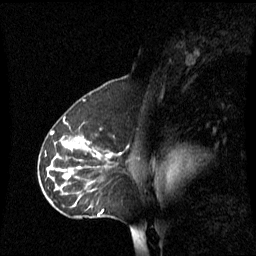
Breast MRI (dynamic contrast-enhanced), one sagittal slice; position 39 of 60 along the scan axis; dynamic contrast-enhanced series, image 2 of 3 at this slice position (ordered by acquisition); 1.5 T; TE 4.2 ms, TR 8.4 ms; 256 × 256 image matrix. Female patient, age 45 years. Case-level facts recorded for this patient, not image findings: setting: breast cancer imaged before/during neoadjuvant chemotherapy; receptor status: HR-positive, HER2-negative.
Structures marked on this image (semi-automatically segmented with operator editing):
- analysis volume of interest (the breast-tissue region the enhancement analysis was run in; not a lesion): box from (x=38, y=122) to (x=123, y=219) px
- tumour enhancement mask (voxels above the 70 % enhancement threshold inside the analysis volume of interest): (x=98, y=152)–(x=101, y=217)